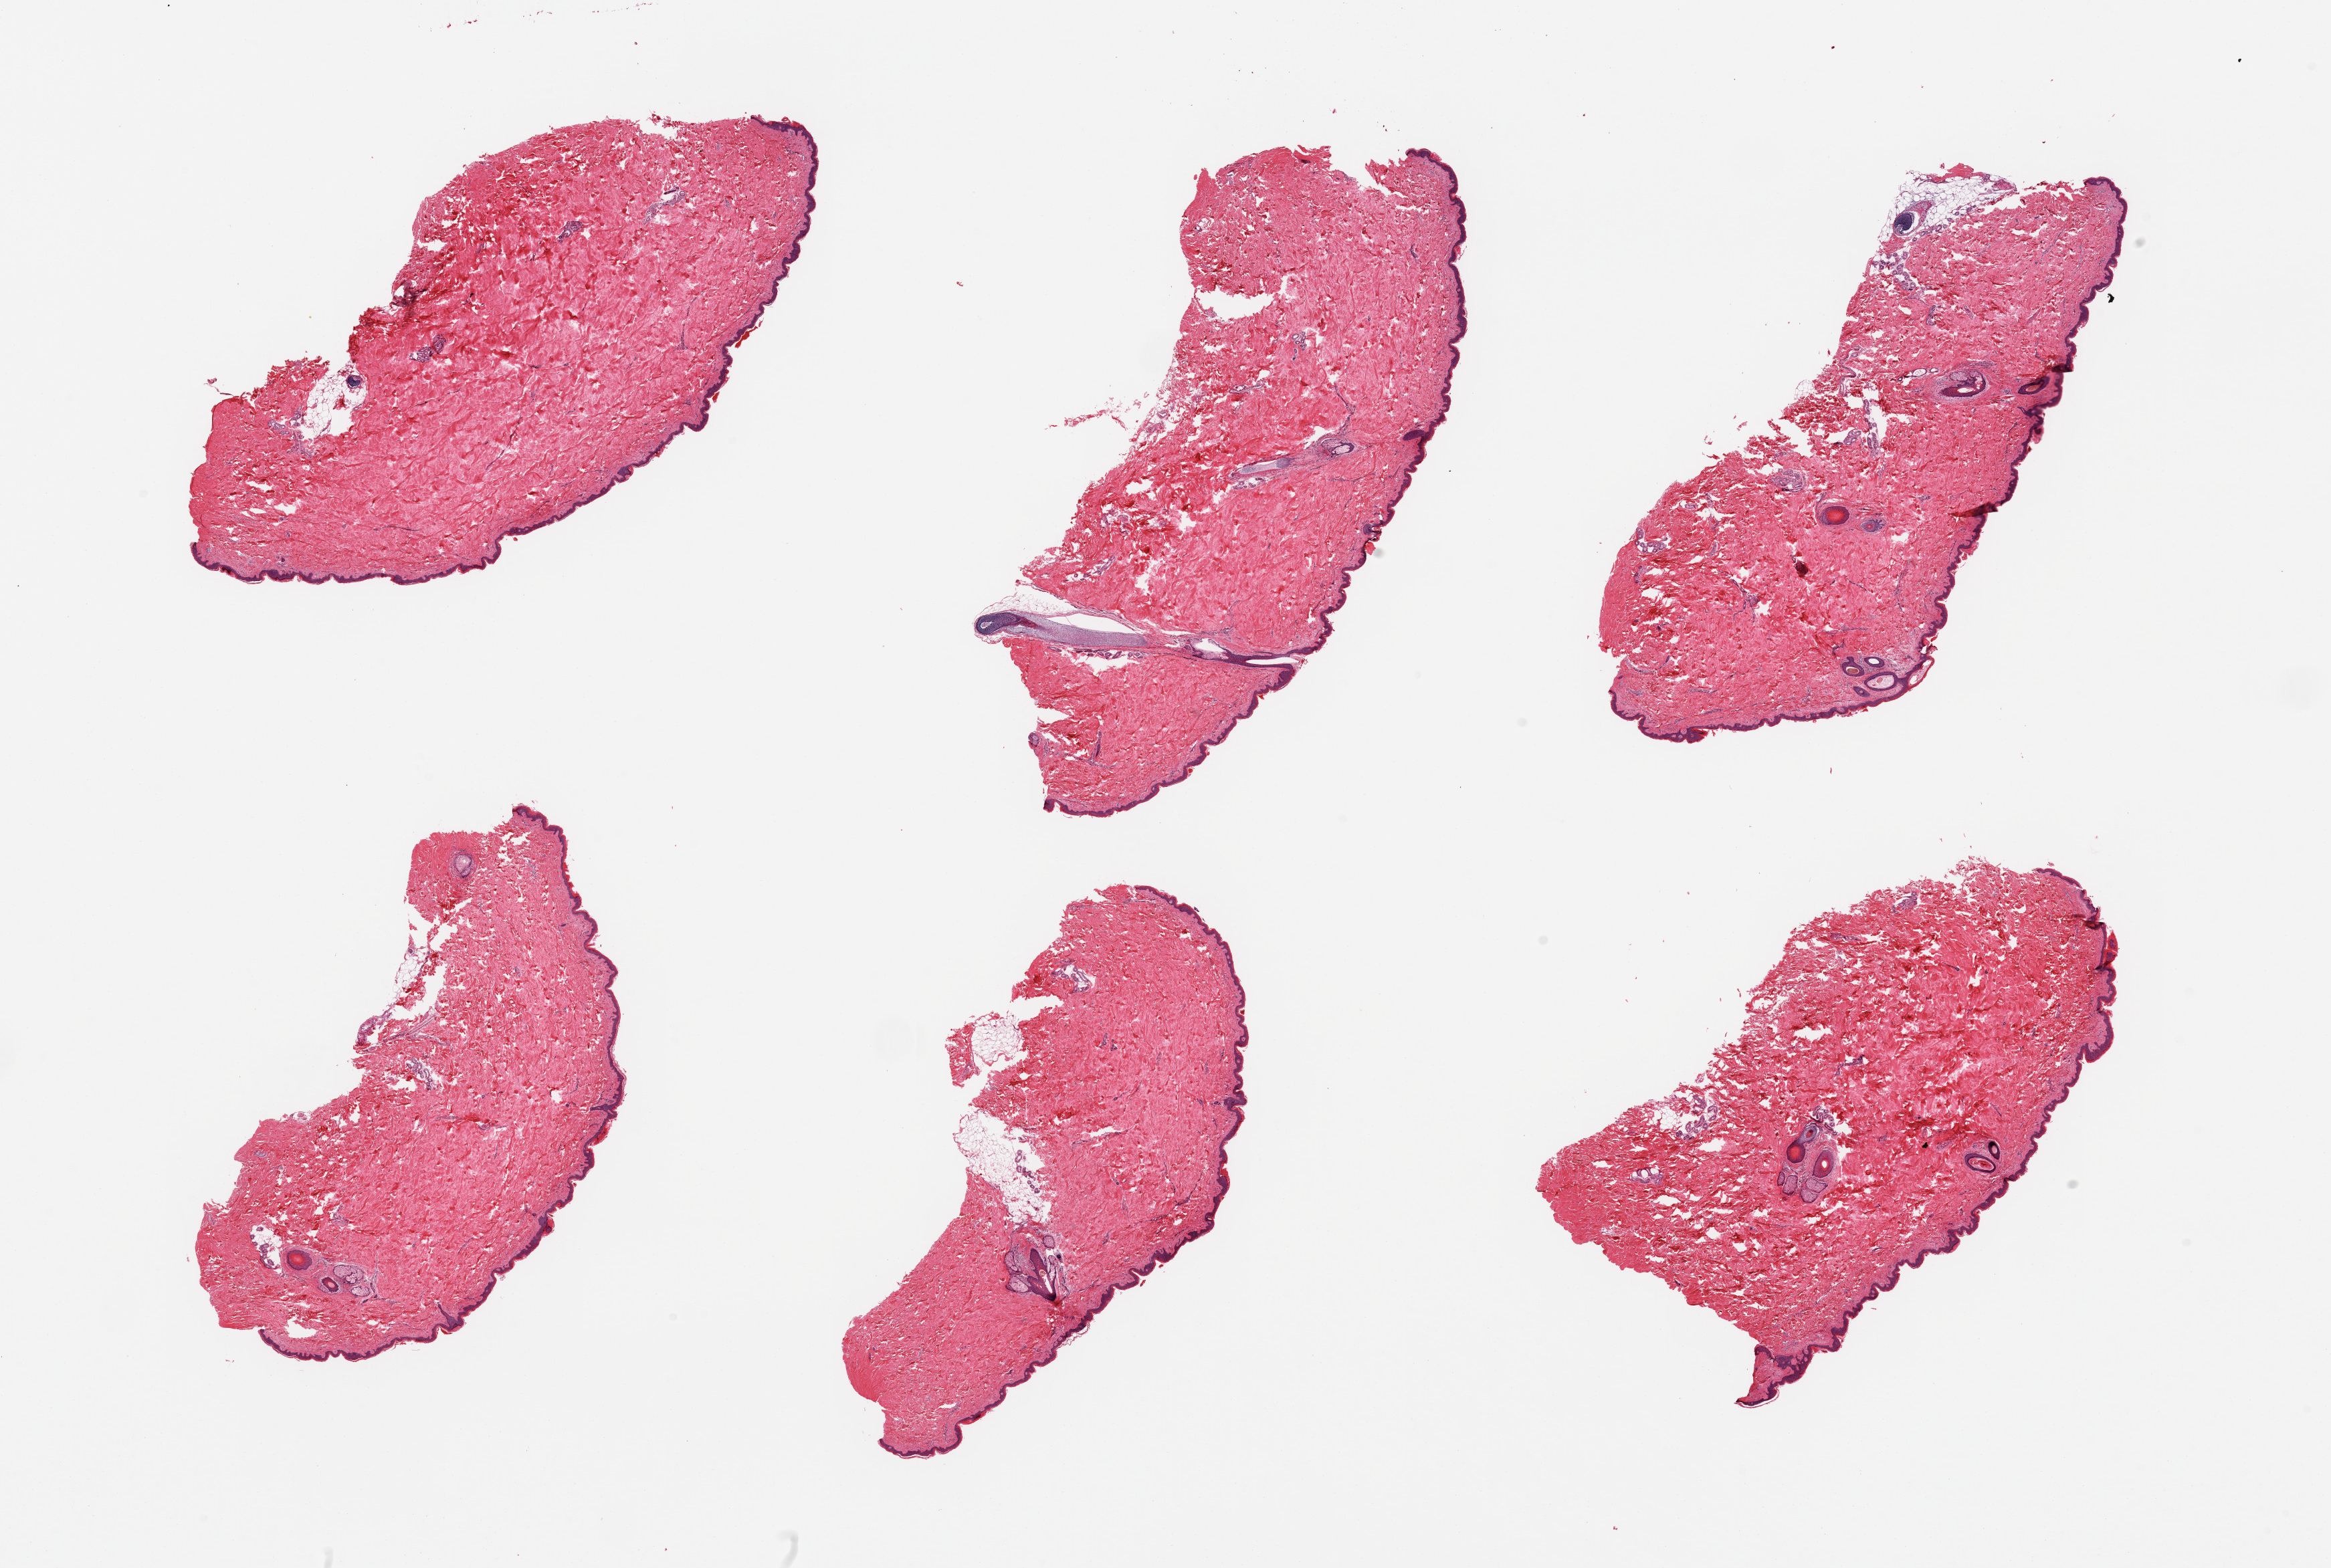
Whole-slide image, haematoxylin and eosin stain — whole scanned area (about 27.6 x 18.5 mm, acquisition: 20x scan) shown as a low-resolution overview, PAXgene-fixed, paraffin-embedded tissue, sampled site (target tissue): skin of suprapubic region, tissue donor sample.
Review note (as recorded): 6 pieces; well trimmed; 5% dermal fat.